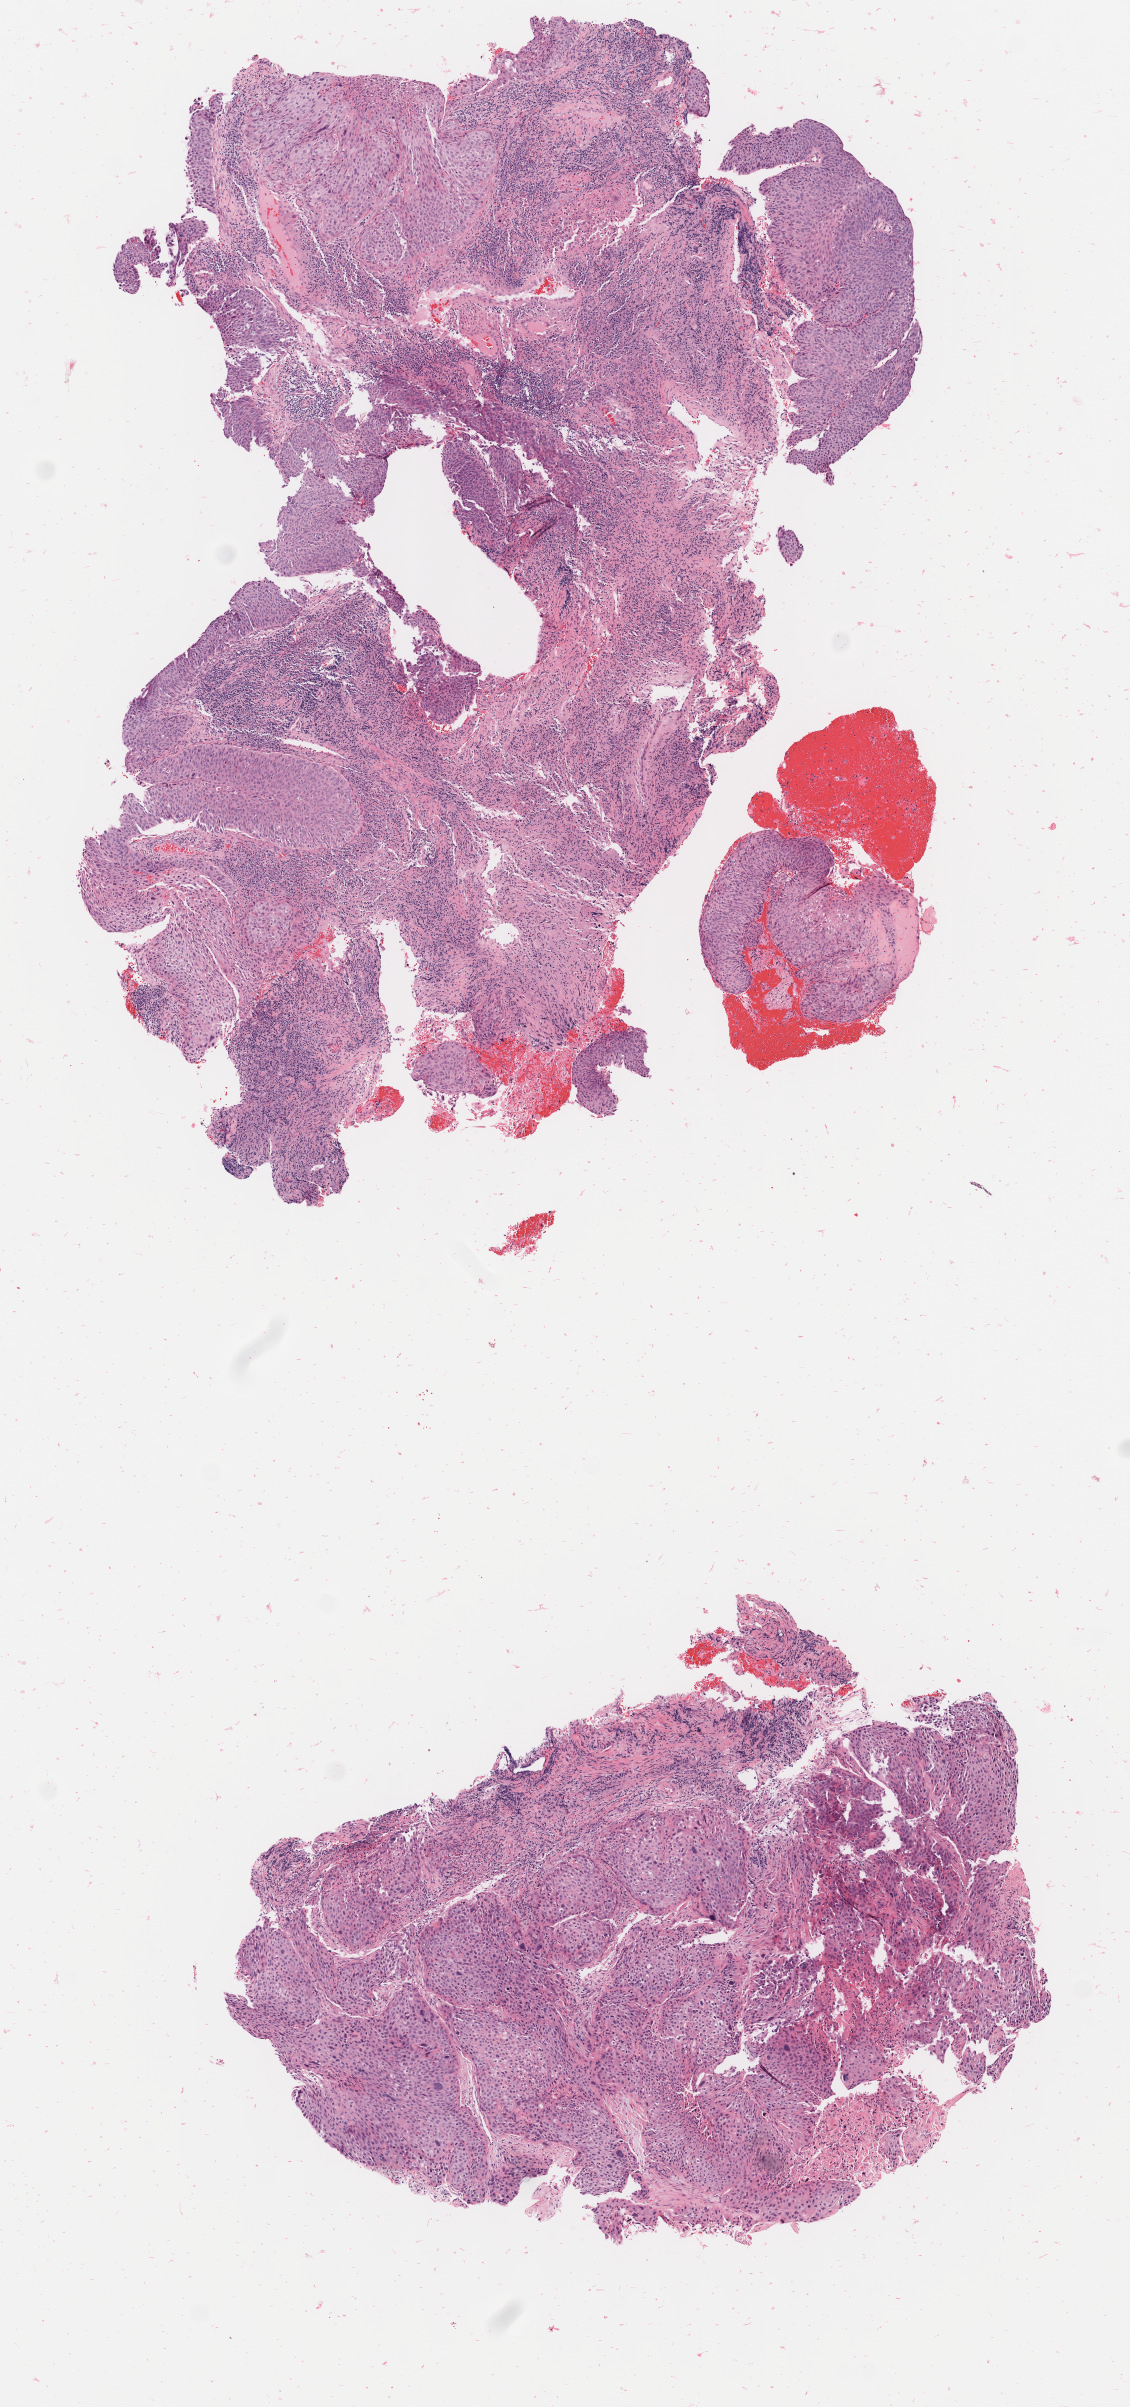
Whole-slide image, hematoxylin and eosin (H&E) stain, low-resolution overview of the scanned area, about 4.5 x 9.6 mm, tumor tissue, anatomic site: cervix. Patient female; age 51 years.
Diagnosis: Squamous cell carcinoma, large cell, nonkeratinizing, NOS.